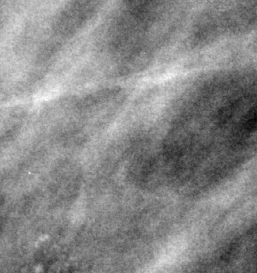
Crop from a digitized film mammogram around one marked abnormality; right breast; MLO view; BI-RADS breast density category 3 (scale 1–4).
- Marked abnormality: calcifications, morphology amorphous / pleomorphic, distribution clustered; BI-RADS assessment category 4; pathology result (as recorded, not read from the image): benign.